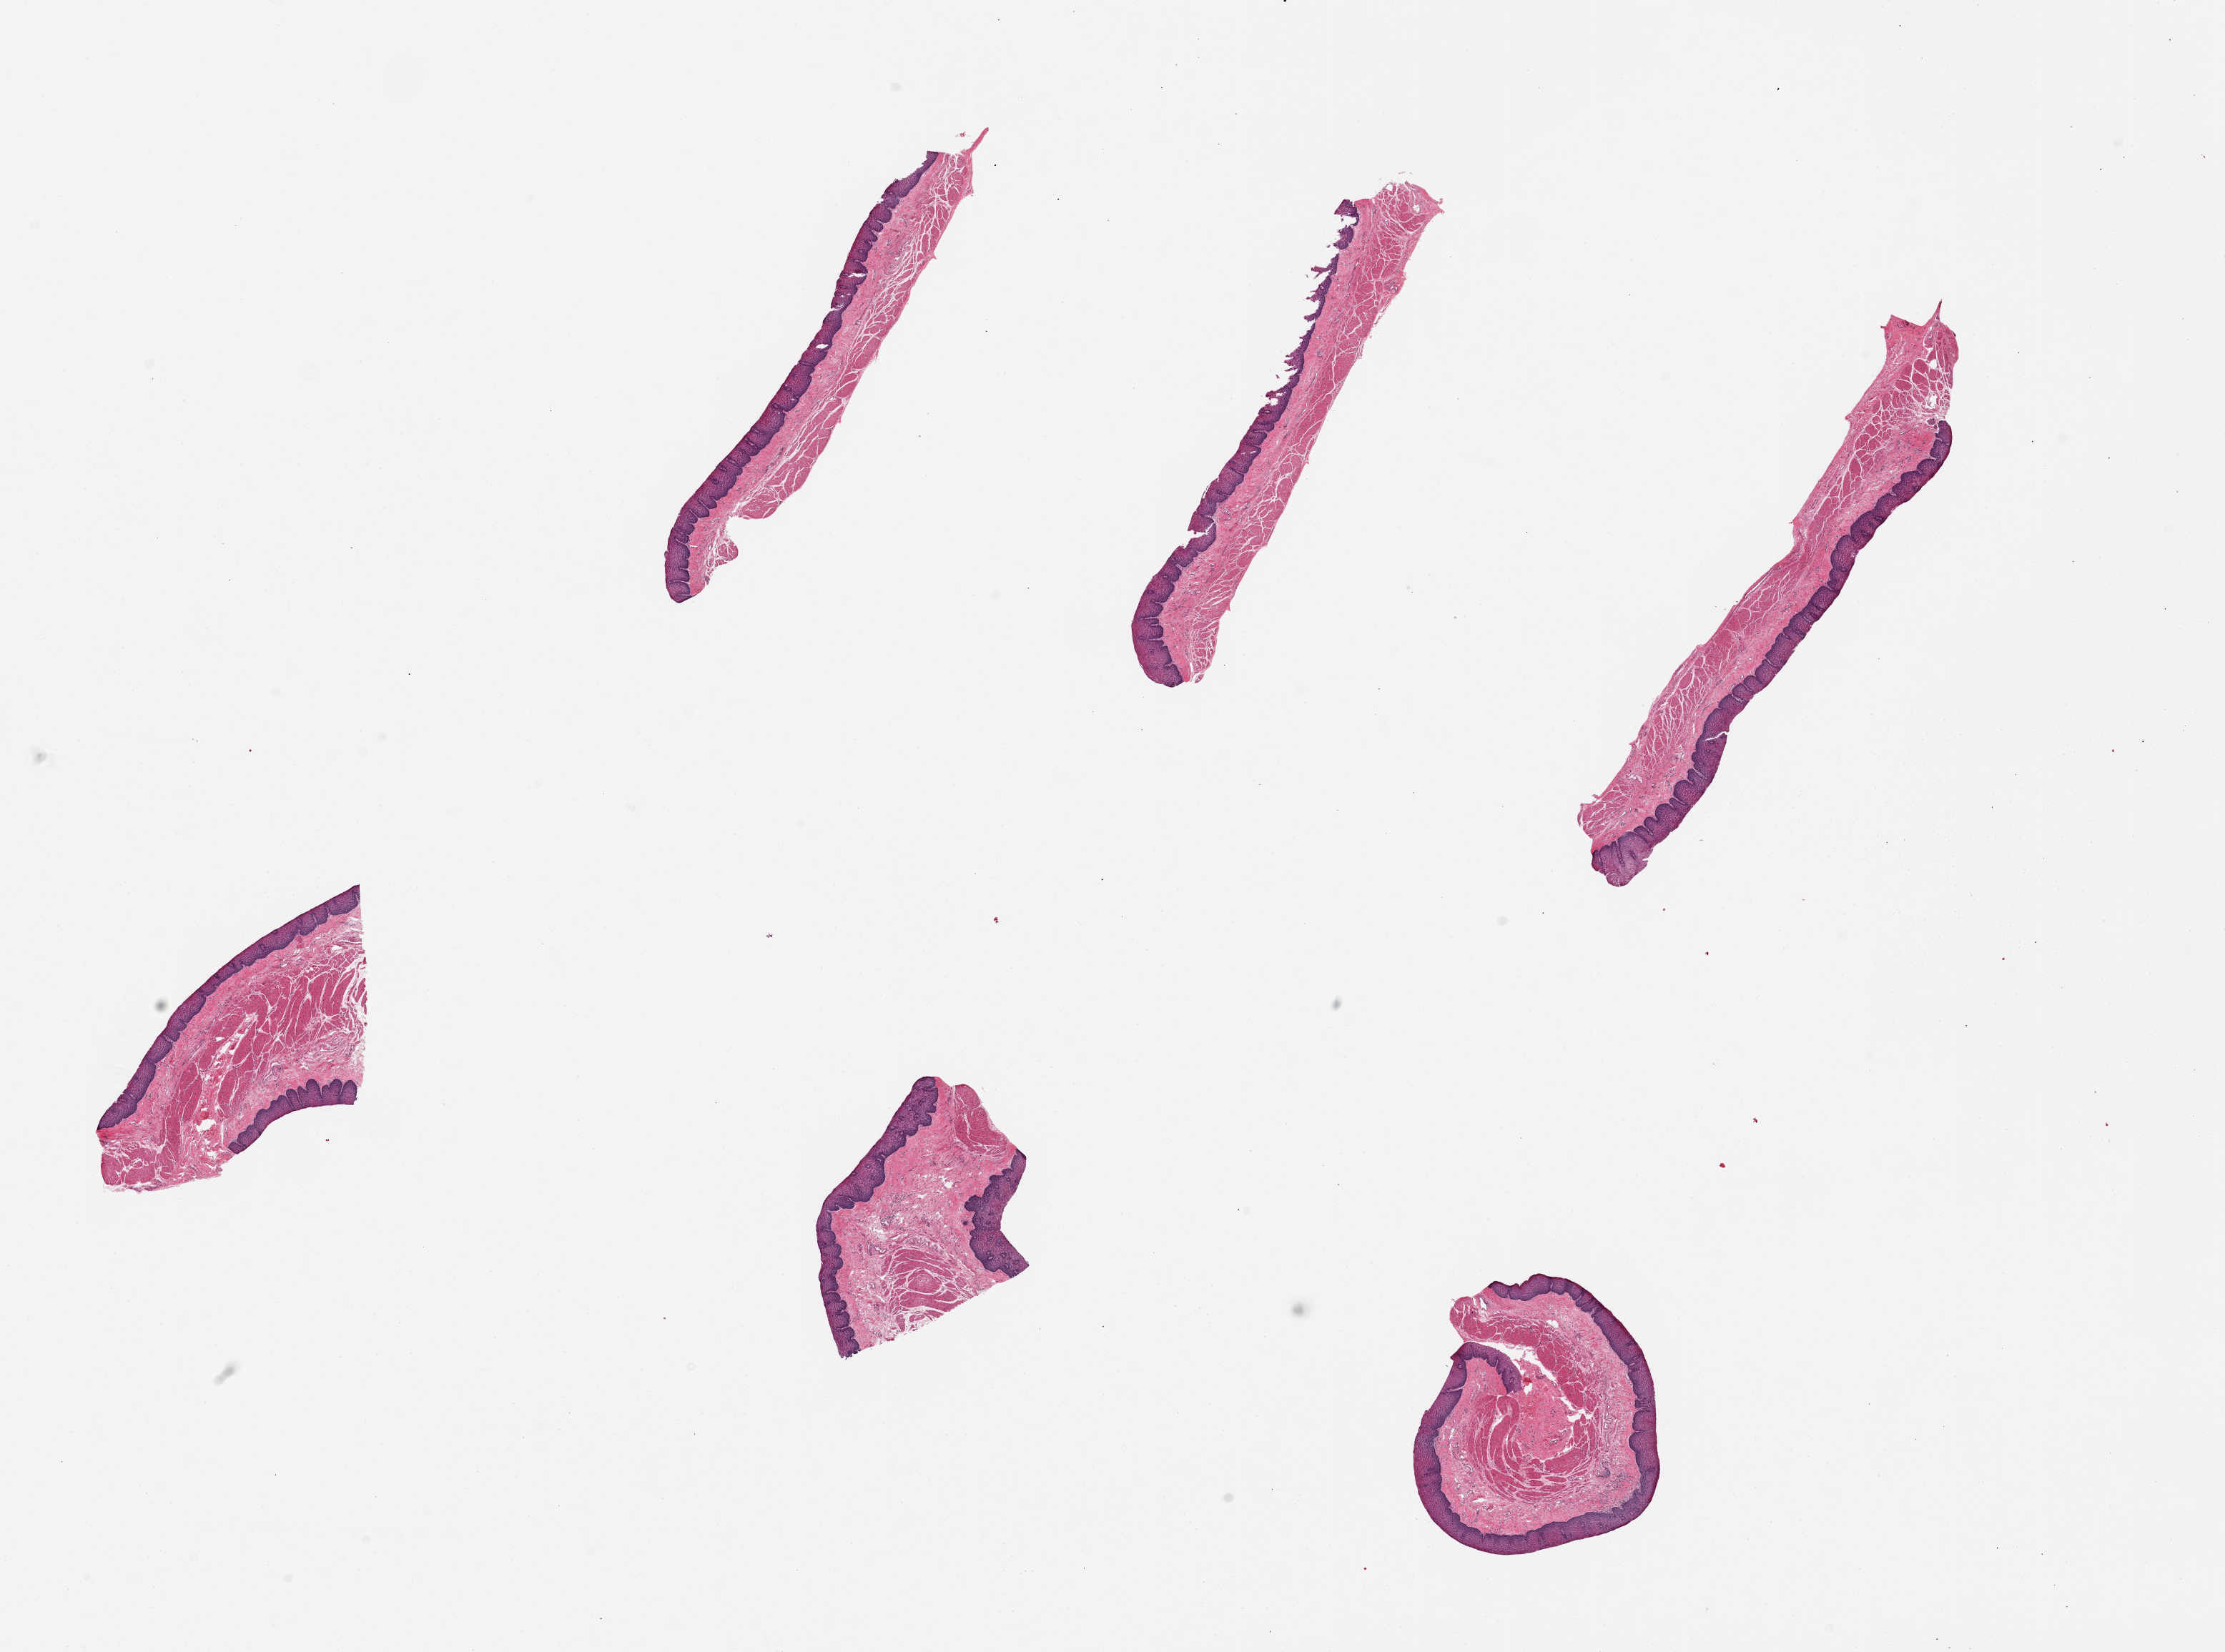
Digitized H&E-stained section — shown as a low-resolution overview of the whole scanned area (about 24.6 x 18.3 mm, from a 20x scan). PAXgene-fixed, paraffin-embedded tissue. Section of esophageal mucous membrane (target tissue). Donor tissue sample. Donor: female.
Review note (as recorded): 1 piece, 3x1.5mm; squamous mucosa is ~30% thickness.